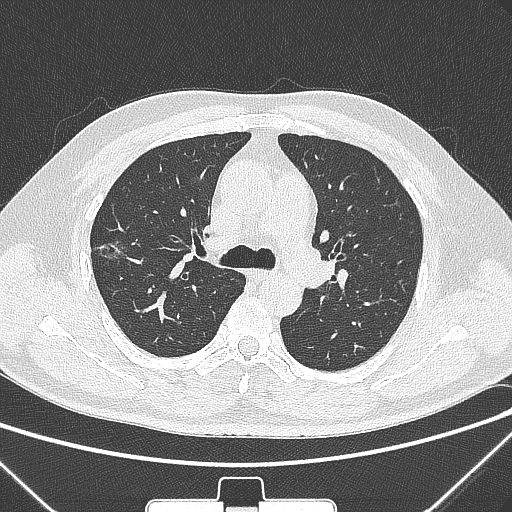
Chest CT, one axial slice. Position 202 of 320 along the scan axis. Lung window (W 1500 / L -600 HU). 1 mm slice thickness. 512 × 512 image matrix. Male patient, age 58 years. Case-level facts recorded for this patient, not image findings: clinical TNM (as recorded): T1c N0 M0.
Annotated regions visible in this slice (rectangle marked by the reading radiologist):
- lung tumour (recorded histology: adenocarcinoma): bounding box <92,231,140,272> (left, top, right, bottom; pixels)